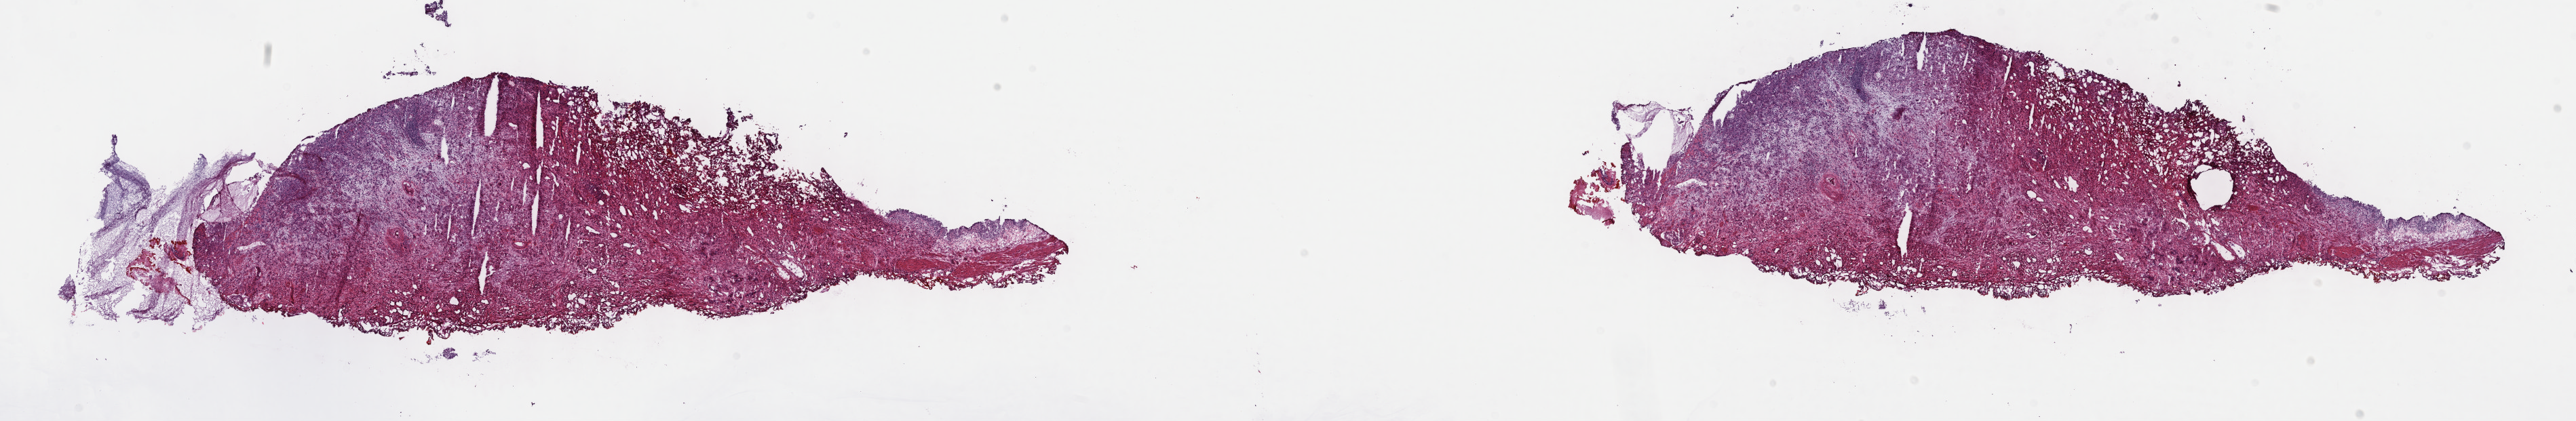
Digitized H&E-stained tissue section (whole slide) — low-resolution overview of the scanned area, about 30.7 x 5.0 mm, frozen section, bladder, primary tumour sample. Female, age 64 years at initial diagnosis. Histologic grade: high grade. Slide review estimates, as recorded: tumour cells 90%, tumour nuclei 70%, normal cells 10%, stromal cells 0%, necrosis 0%. Inflammatory infiltration, as recorded: lymphocyte infiltration 2%, monocyte infiltration 0%, neutrophil infiltration 0%.
Diagnosis: Transitional cell carcinoma (lateral wall of bladder). AJCC pathologic stage: II (7th edition).